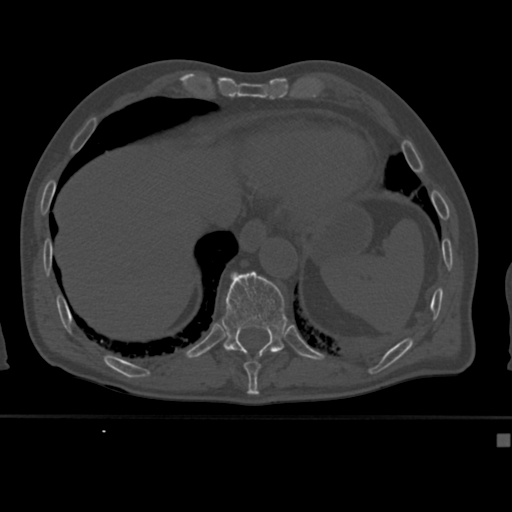
CT including the spine, one axial slice. Position 217 of 430 along the scan axis. Reconstruction kernel Br40s. 120 kVp. Bone window (W 1800 / L 400 HU). 1.5 mm slice thickness. 512 × 512 image matrix, field of view 337 × 337 mm. Patient: male, 64 years. Case-level facts recorded for this patient, not image findings: primary cancer: uterus; vertebrae with lytic lesions (as recorded): T1, T4, T5, T7, L5.
Annotated regions visible in this slice (semi-automatic segmentation, software-assisted and operator-edited):
- T10 vertebra: bounding box (x1, y1, x2, y2) in pixels: (243, 358, 261, 382)
- T11 vertebra: (221, 271, 288, 358)